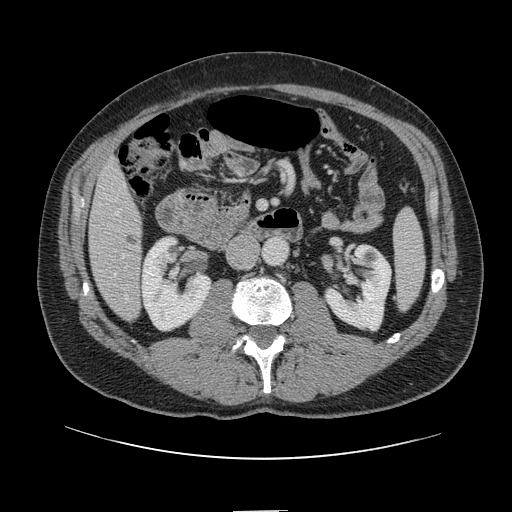
Contrast-enhanced abdominal CT, one axial slice. Slice 31 of 161 in the series (ordered by position). Intravenous contrast given. Soft-tissue window (W 400 / L 40 HU). 2.5 mm slice thickness. 512 × 512 image matrix, field of view 412 × 412 mm. Male patient, age 66 years. From the clinical record (not read from this slice): diagnosis: colorectal cancer liver metastases, imaged before liver resection; multiple liver metastases: no; largest metastasis: 3.5 cm; chemotherapy before resection: yes.
Outlined on this slice (expert manual segmentation):
- hepatic veins: bounding box <115,213,119,275> (left, top, right, bottom; pixels)
- liver: <90,162,143,320>
- planned liver remnant (the part of the liver to remain after resection): <90,162,142,261>